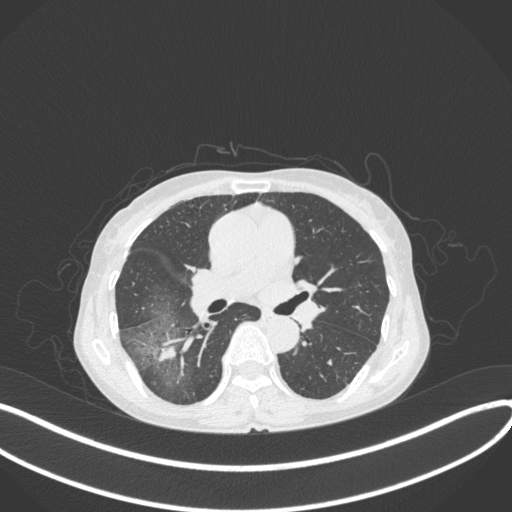
Chest CT, one axial slice; slice 222 of 379 in the series (ordered by position); reconstruction kernel B31f; 120 kVp; lung window (W 1500 / L -600 HU); 512 × 512 image matrix, field of view 400 × 400 mm. Female patient, age 69 years. From the clinical record (not read from this slice): clinical TNM (as recorded): T1b N0 M0.
Structures marked on this image (rectangle marked by the reading radiologist):
- lung tumour (recorded histology: adenocarcinoma): bounding box [x1, y1, x2, y2] px = [151, 344, 182, 367]